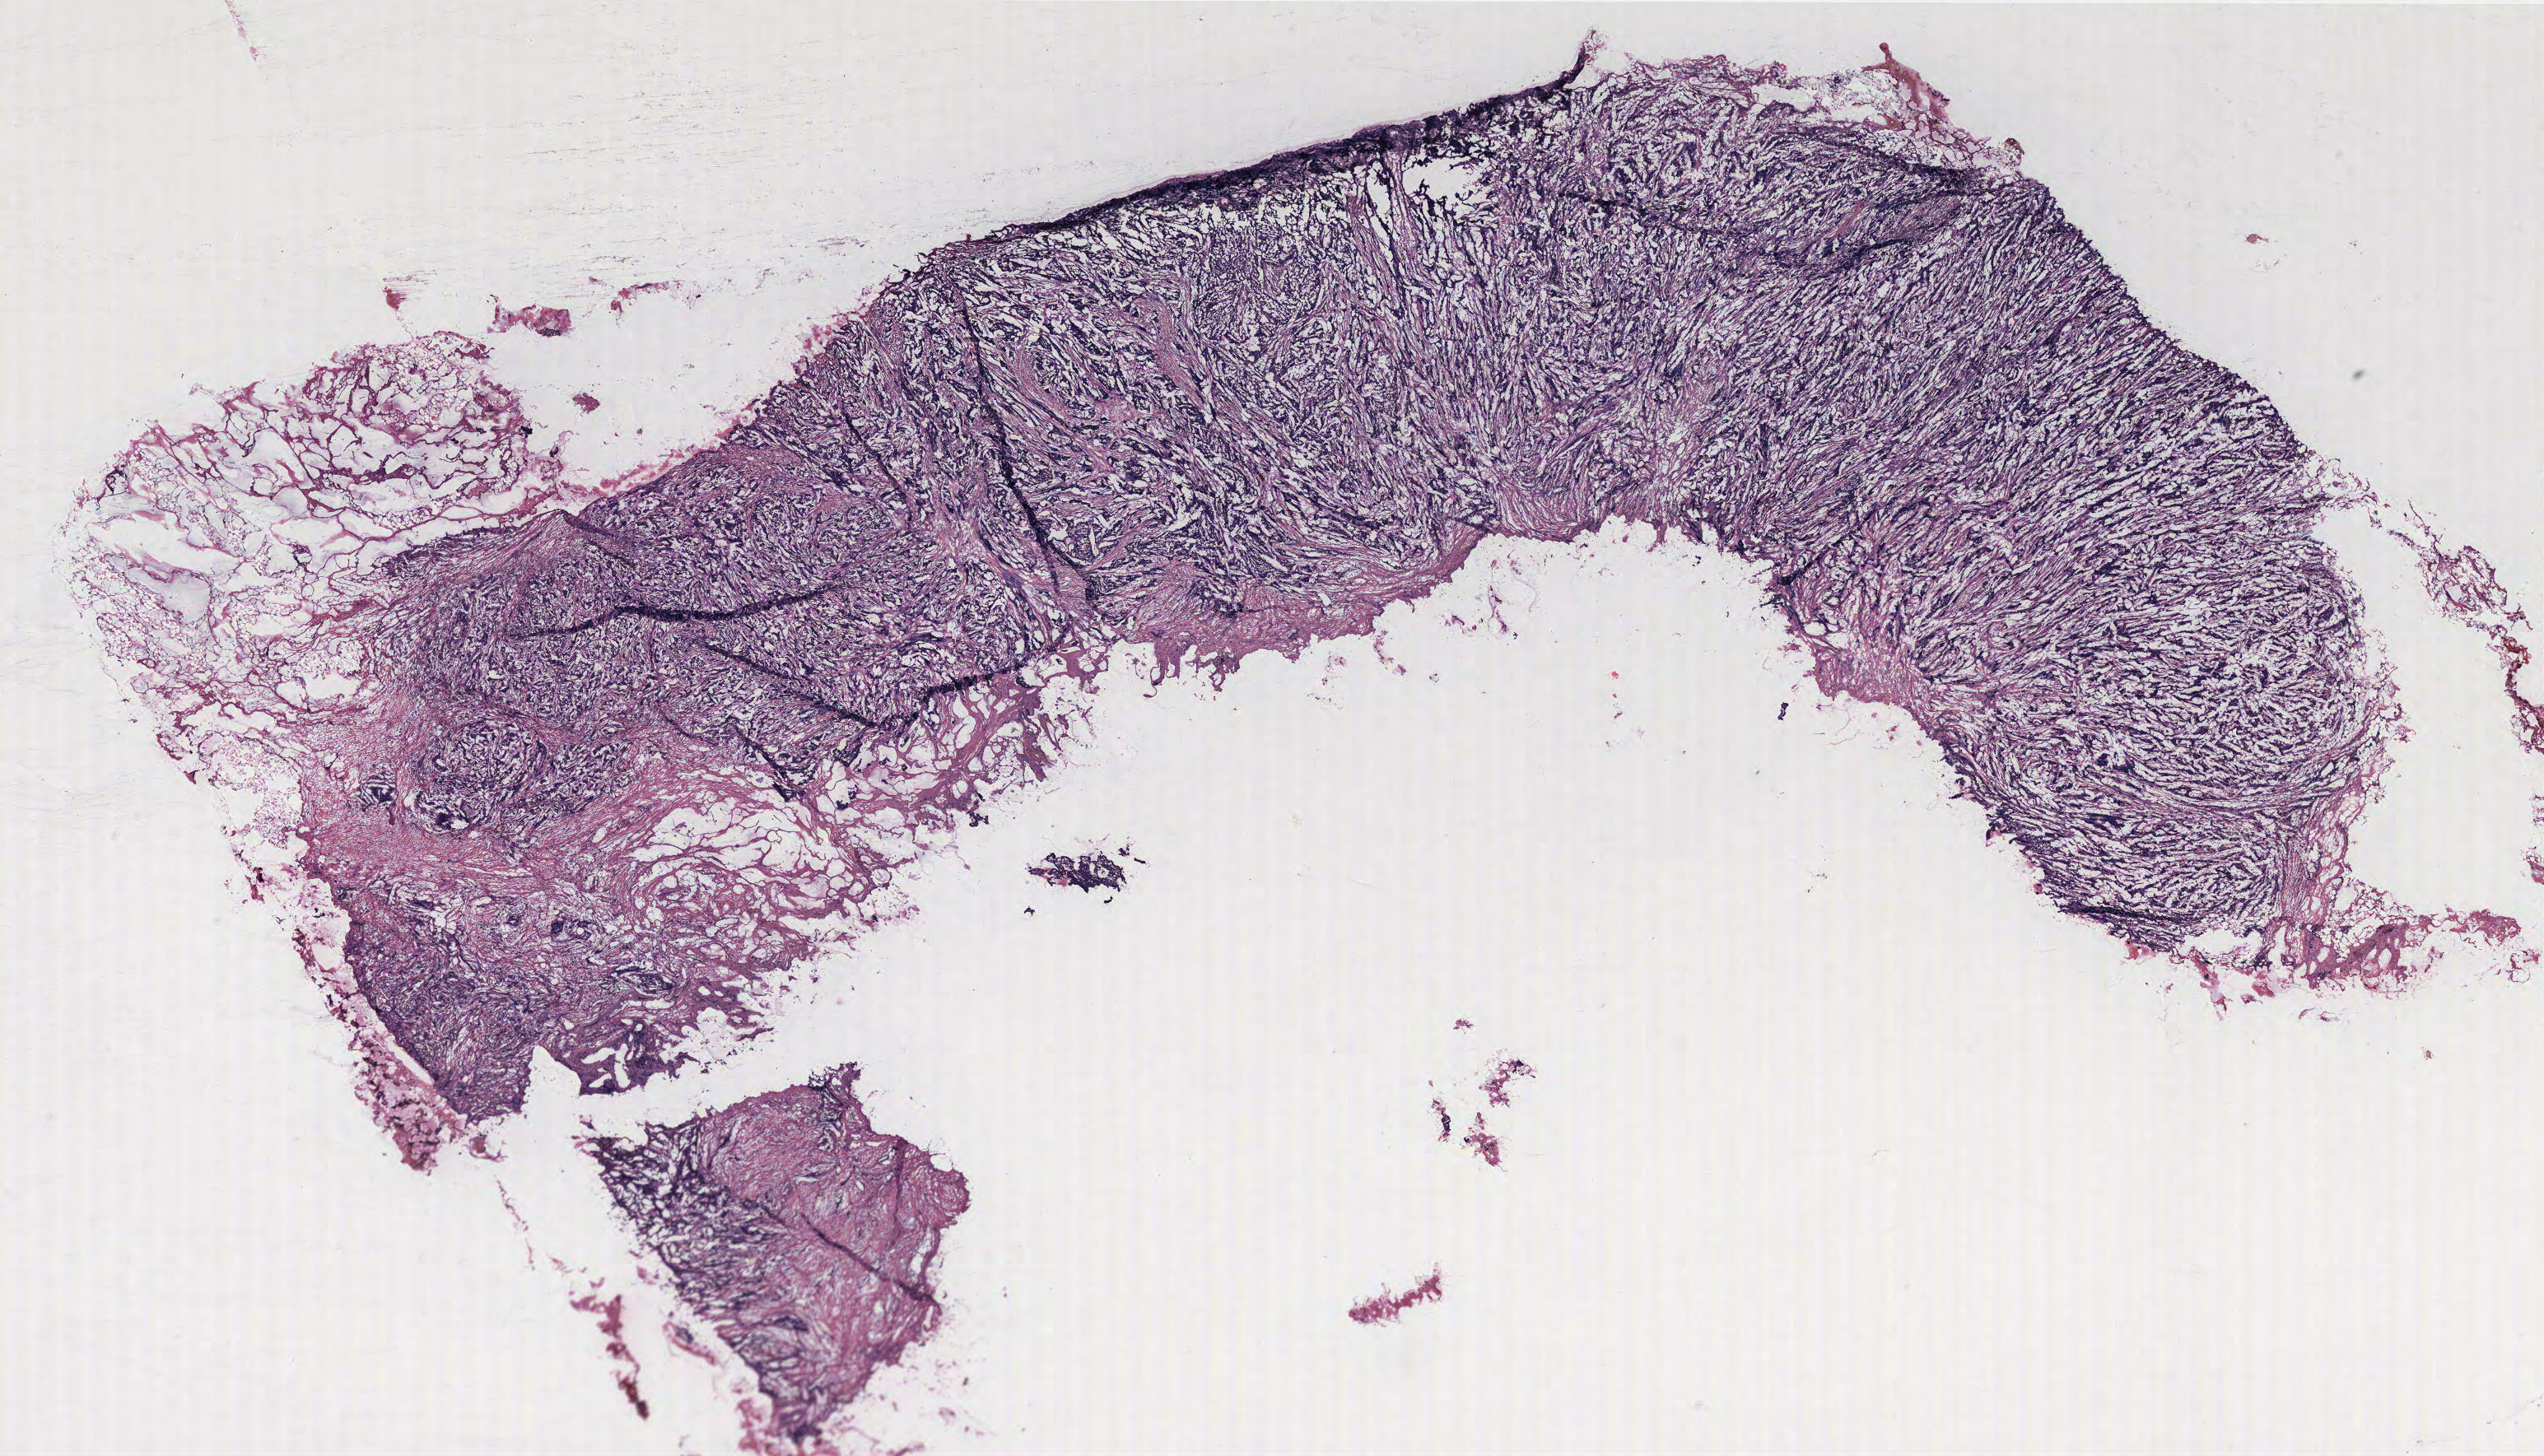
H&E whole-slide image, whole scanned area (about 24.7 x 14.2 mm, from a 40x scan) shown as a low-resolution overview, breast, tissue type not recorded. Female, 45 y/o.
Patient diagnosis: Infiltrating duct carcinoma, NOS.